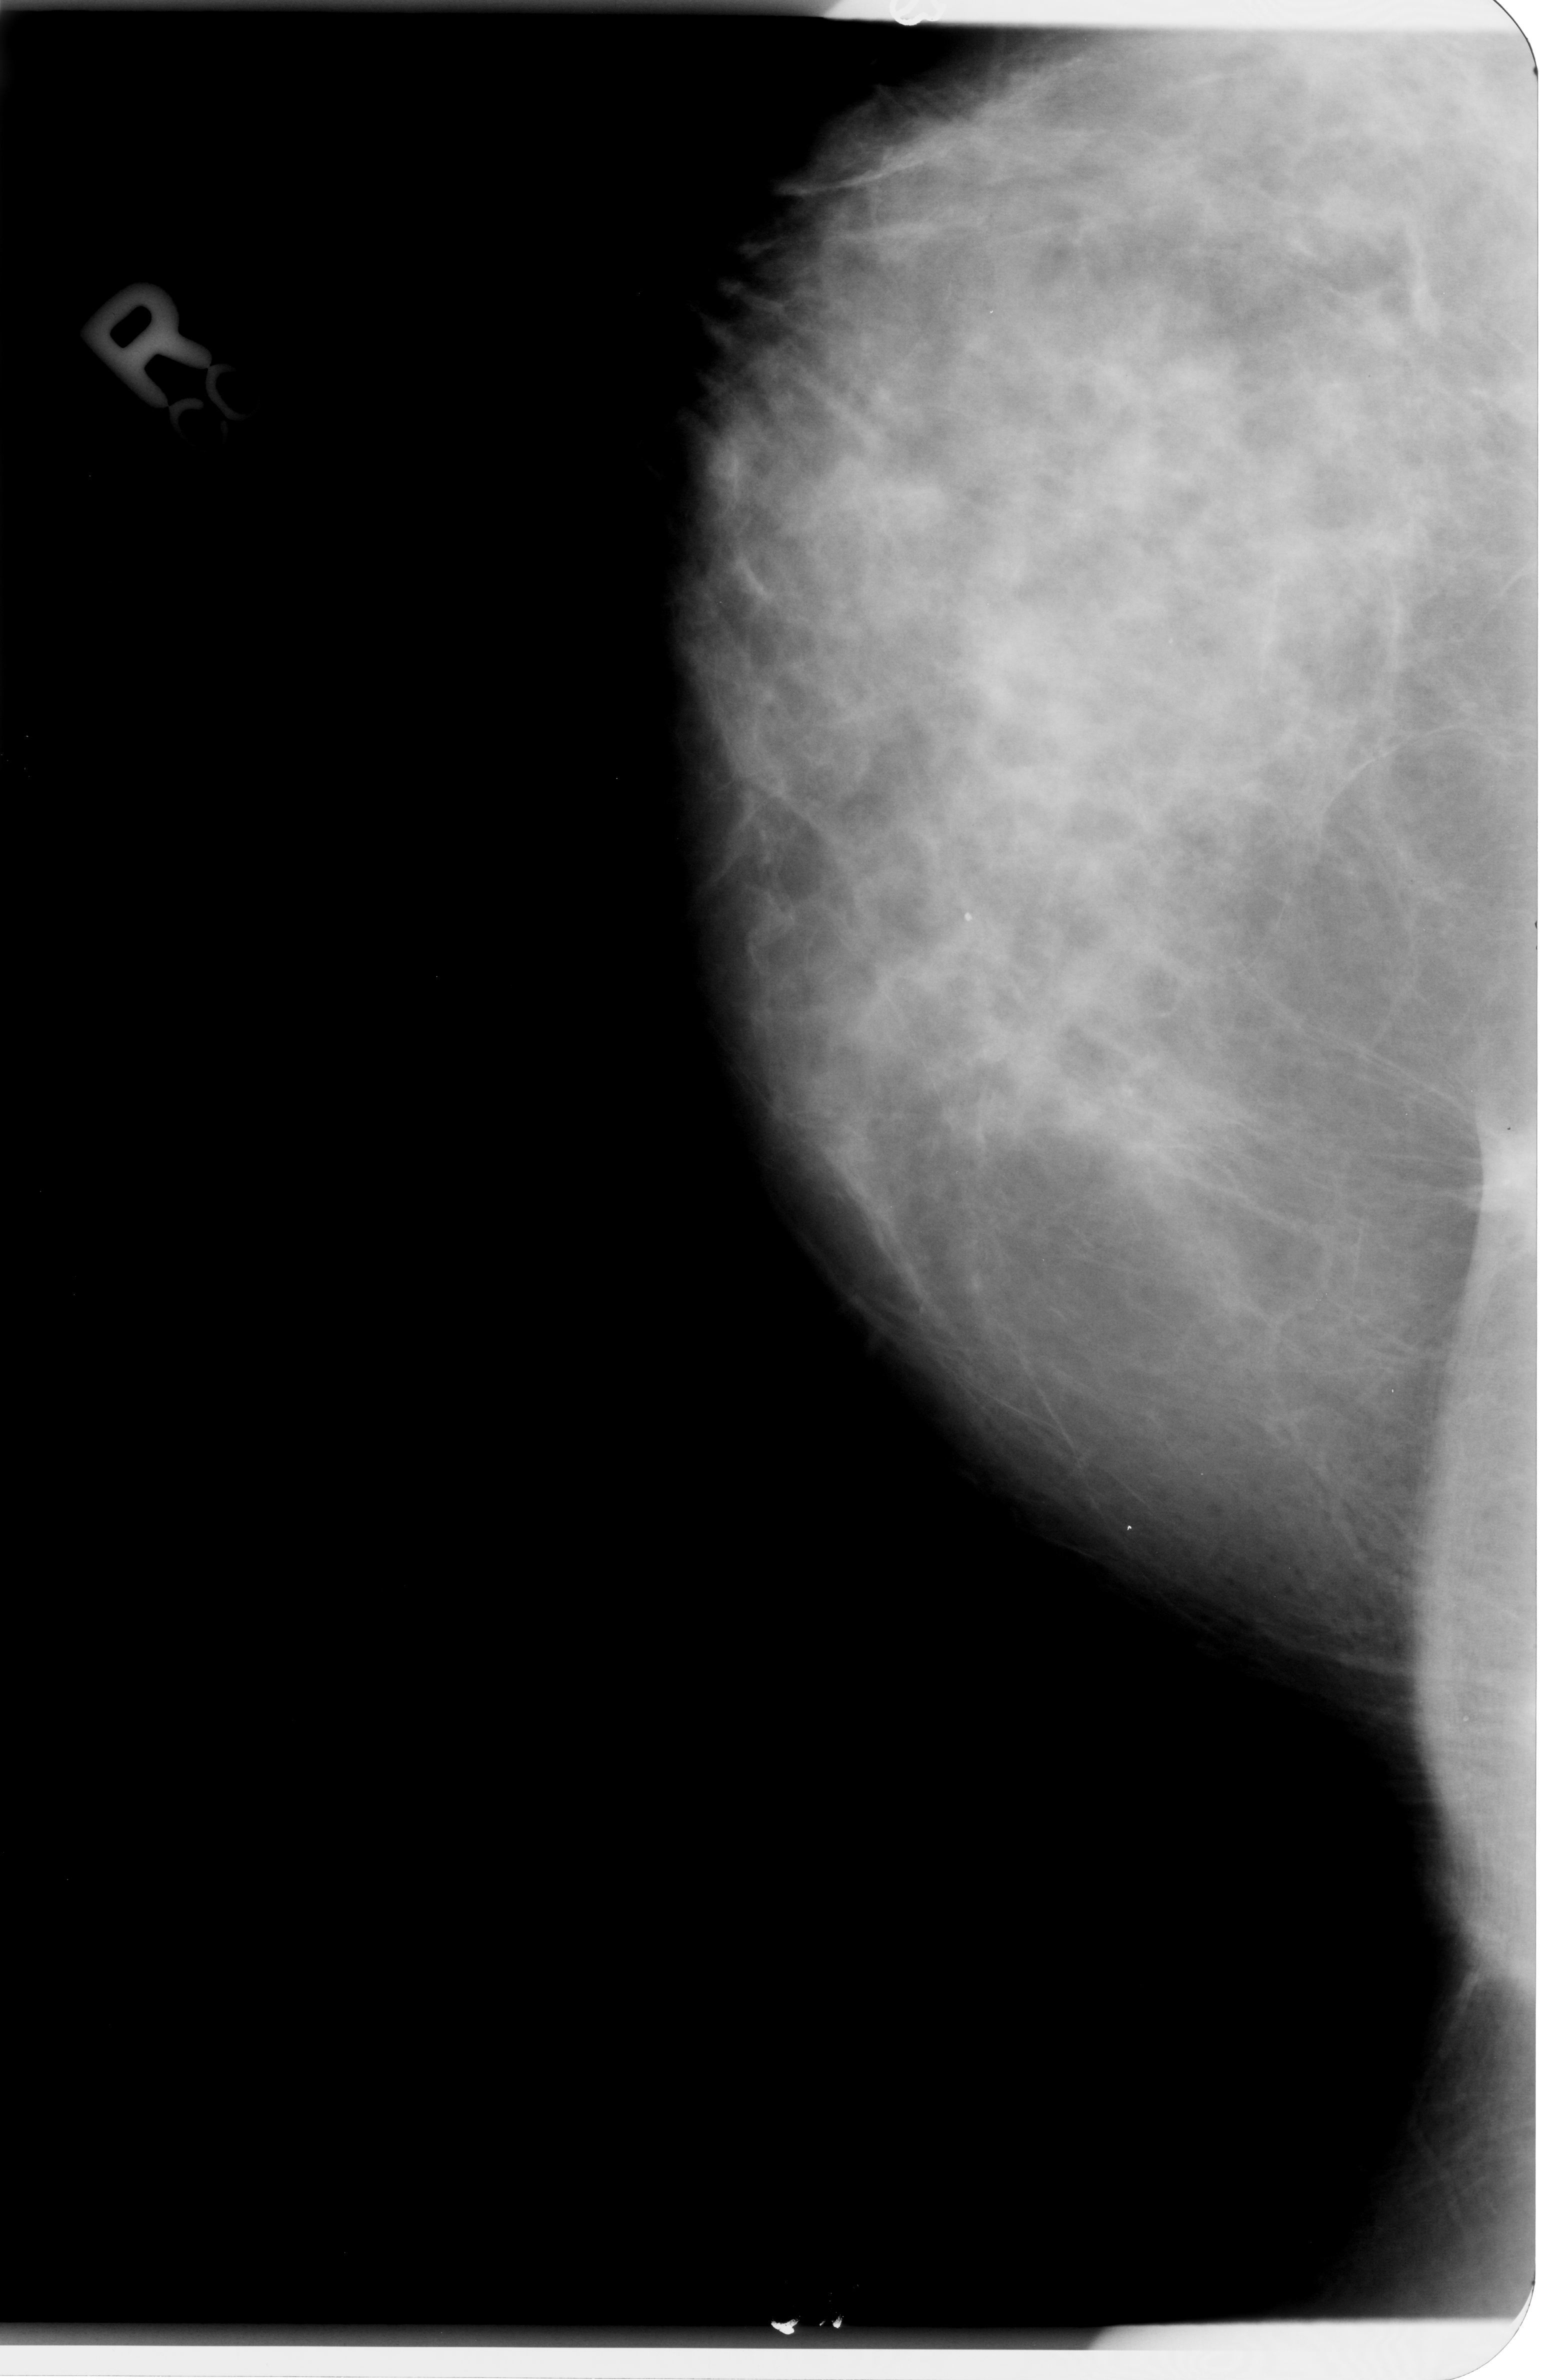
Digitized screen-film mammogram; right breast; craniocaudal (CC) view; breast composition: heterogeneously dense (BI-RADS density category 3 of 4).
- Mass, shape irregular, margins spiculated; BI-RADS assessment category 4; pathology result (as recorded, not read from the image): malignant.